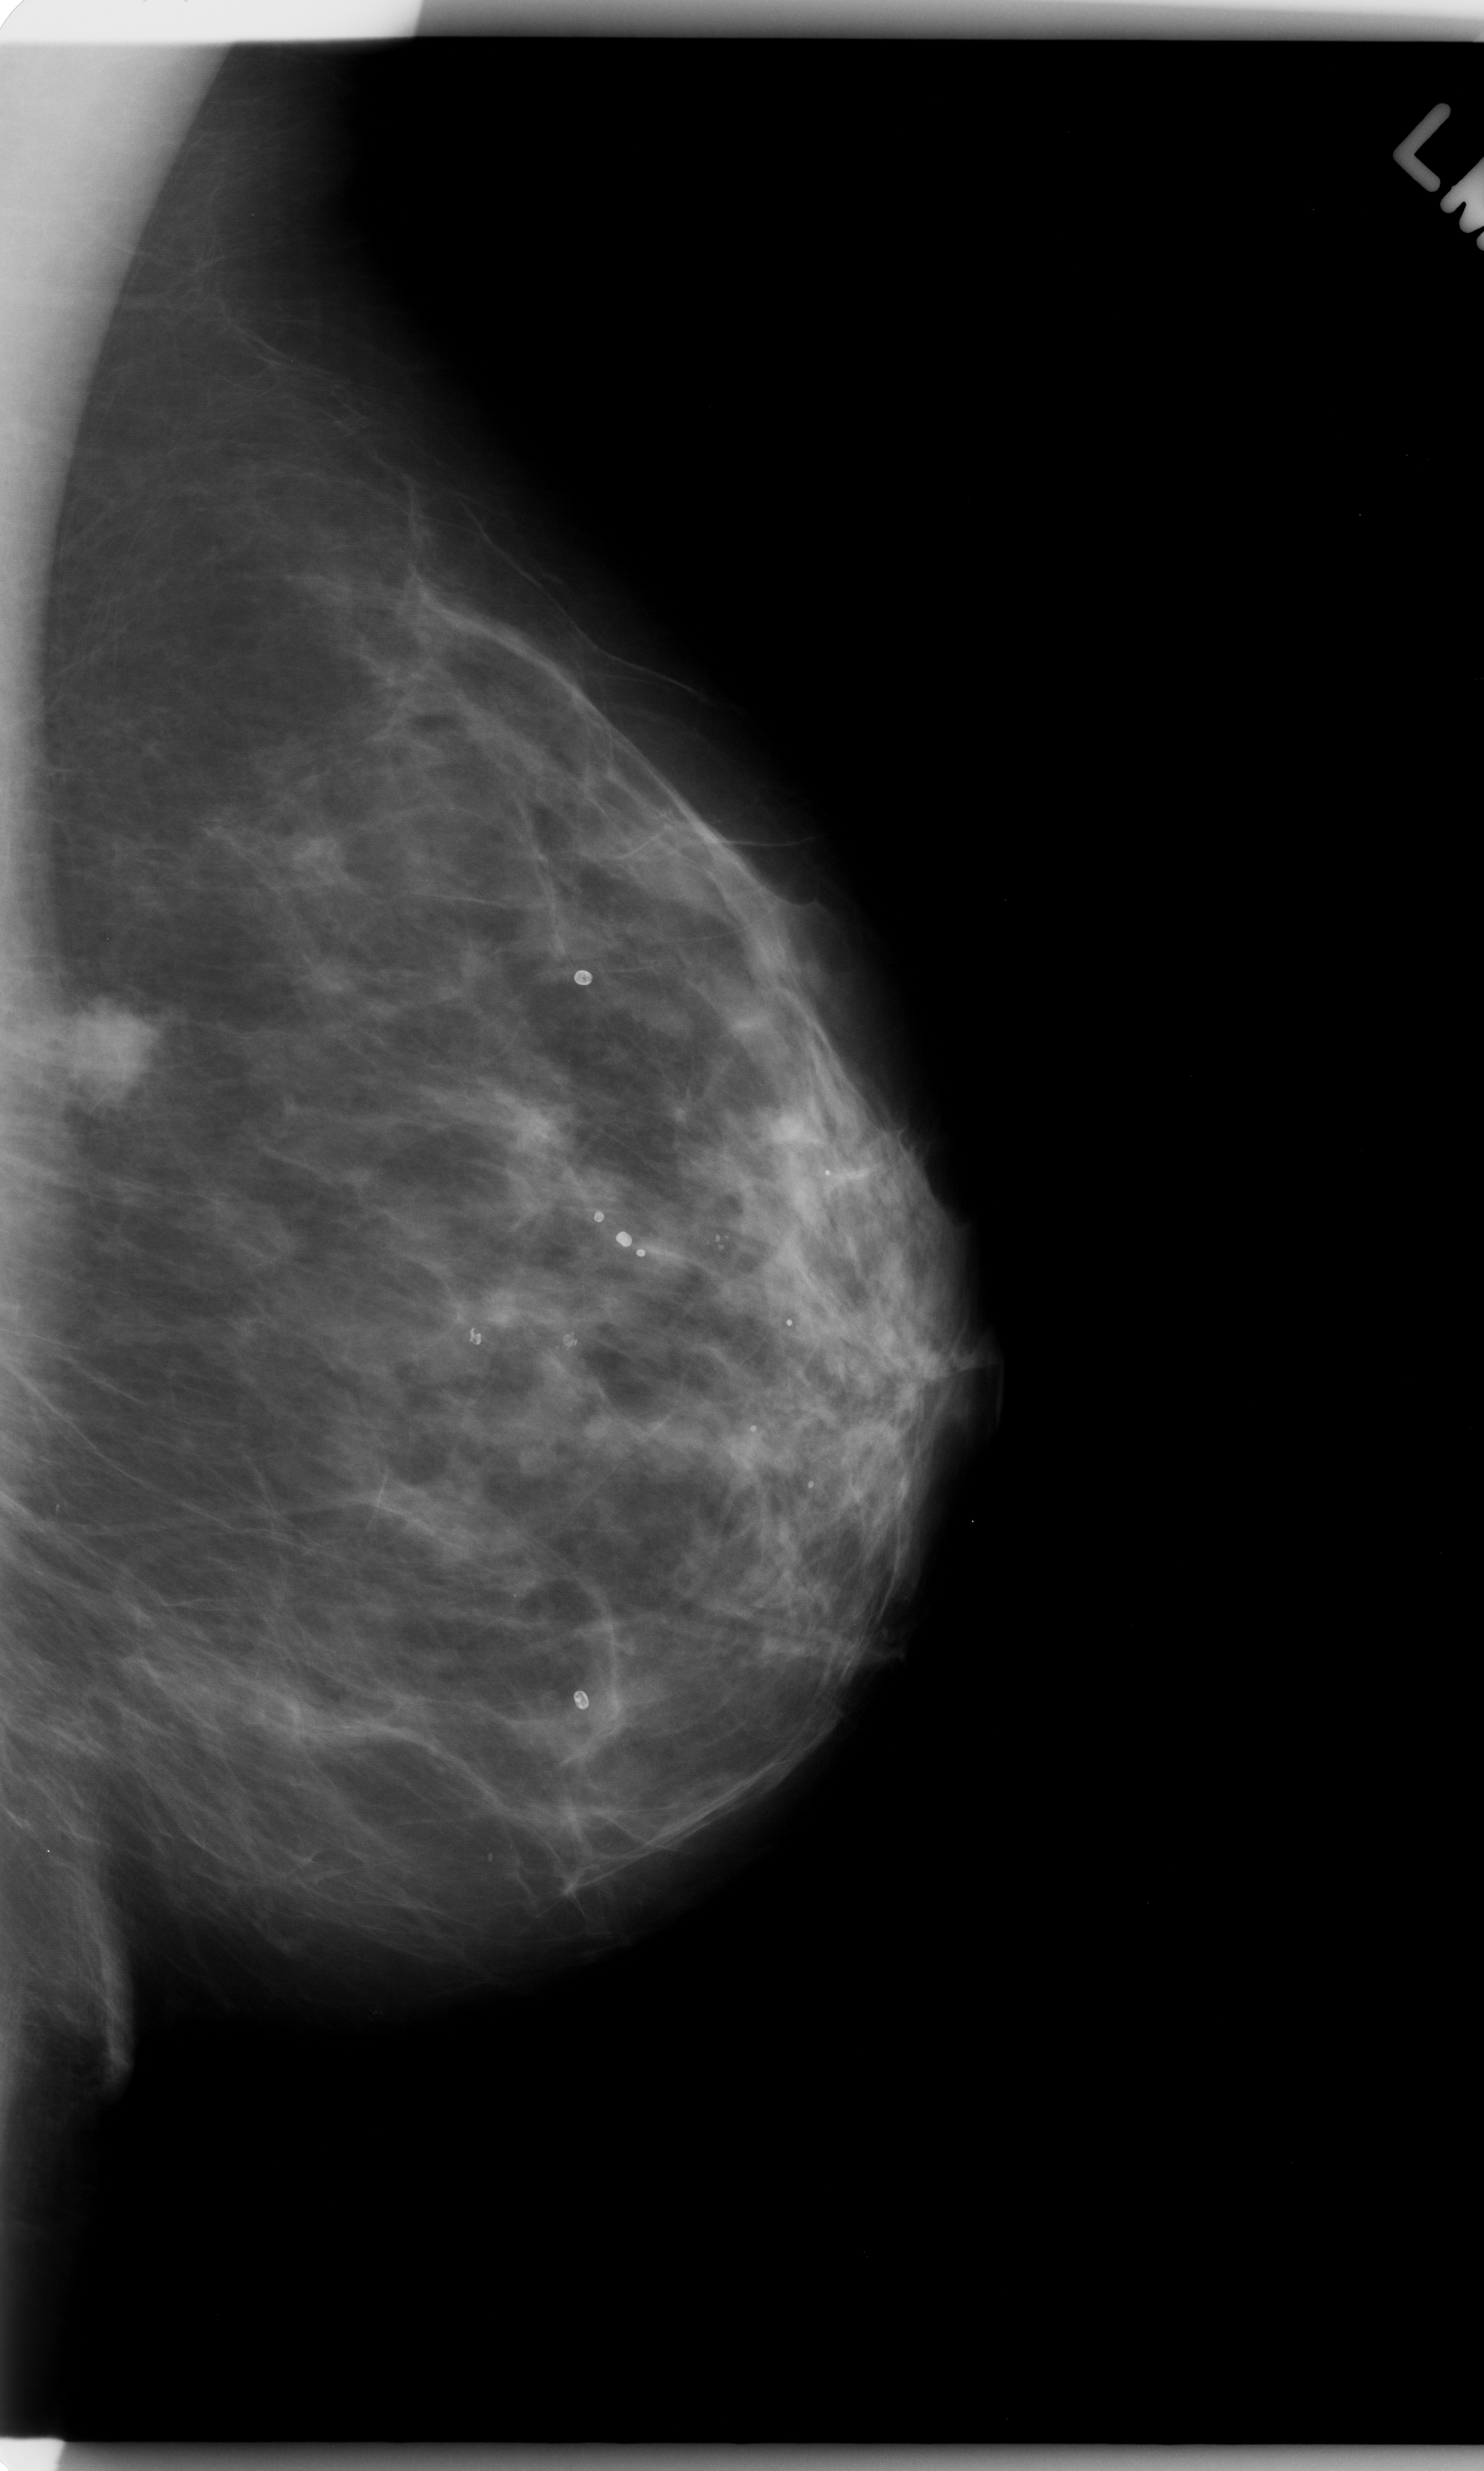
Mammogram (digitized film), left breast, mediolateral oblique (MLO) view, breast composition: scattered fibroglandular densities (BI-RADS density category 2 of 4).
- Abnormality record for this image: mass, shape lobulated, margins microlobulated; BI-RADS assessment category 5; subtlety rating 5 on a 1 (subtle) to 5 (obvious) scale; pathology result (as recorded, not read from the image): malignant.